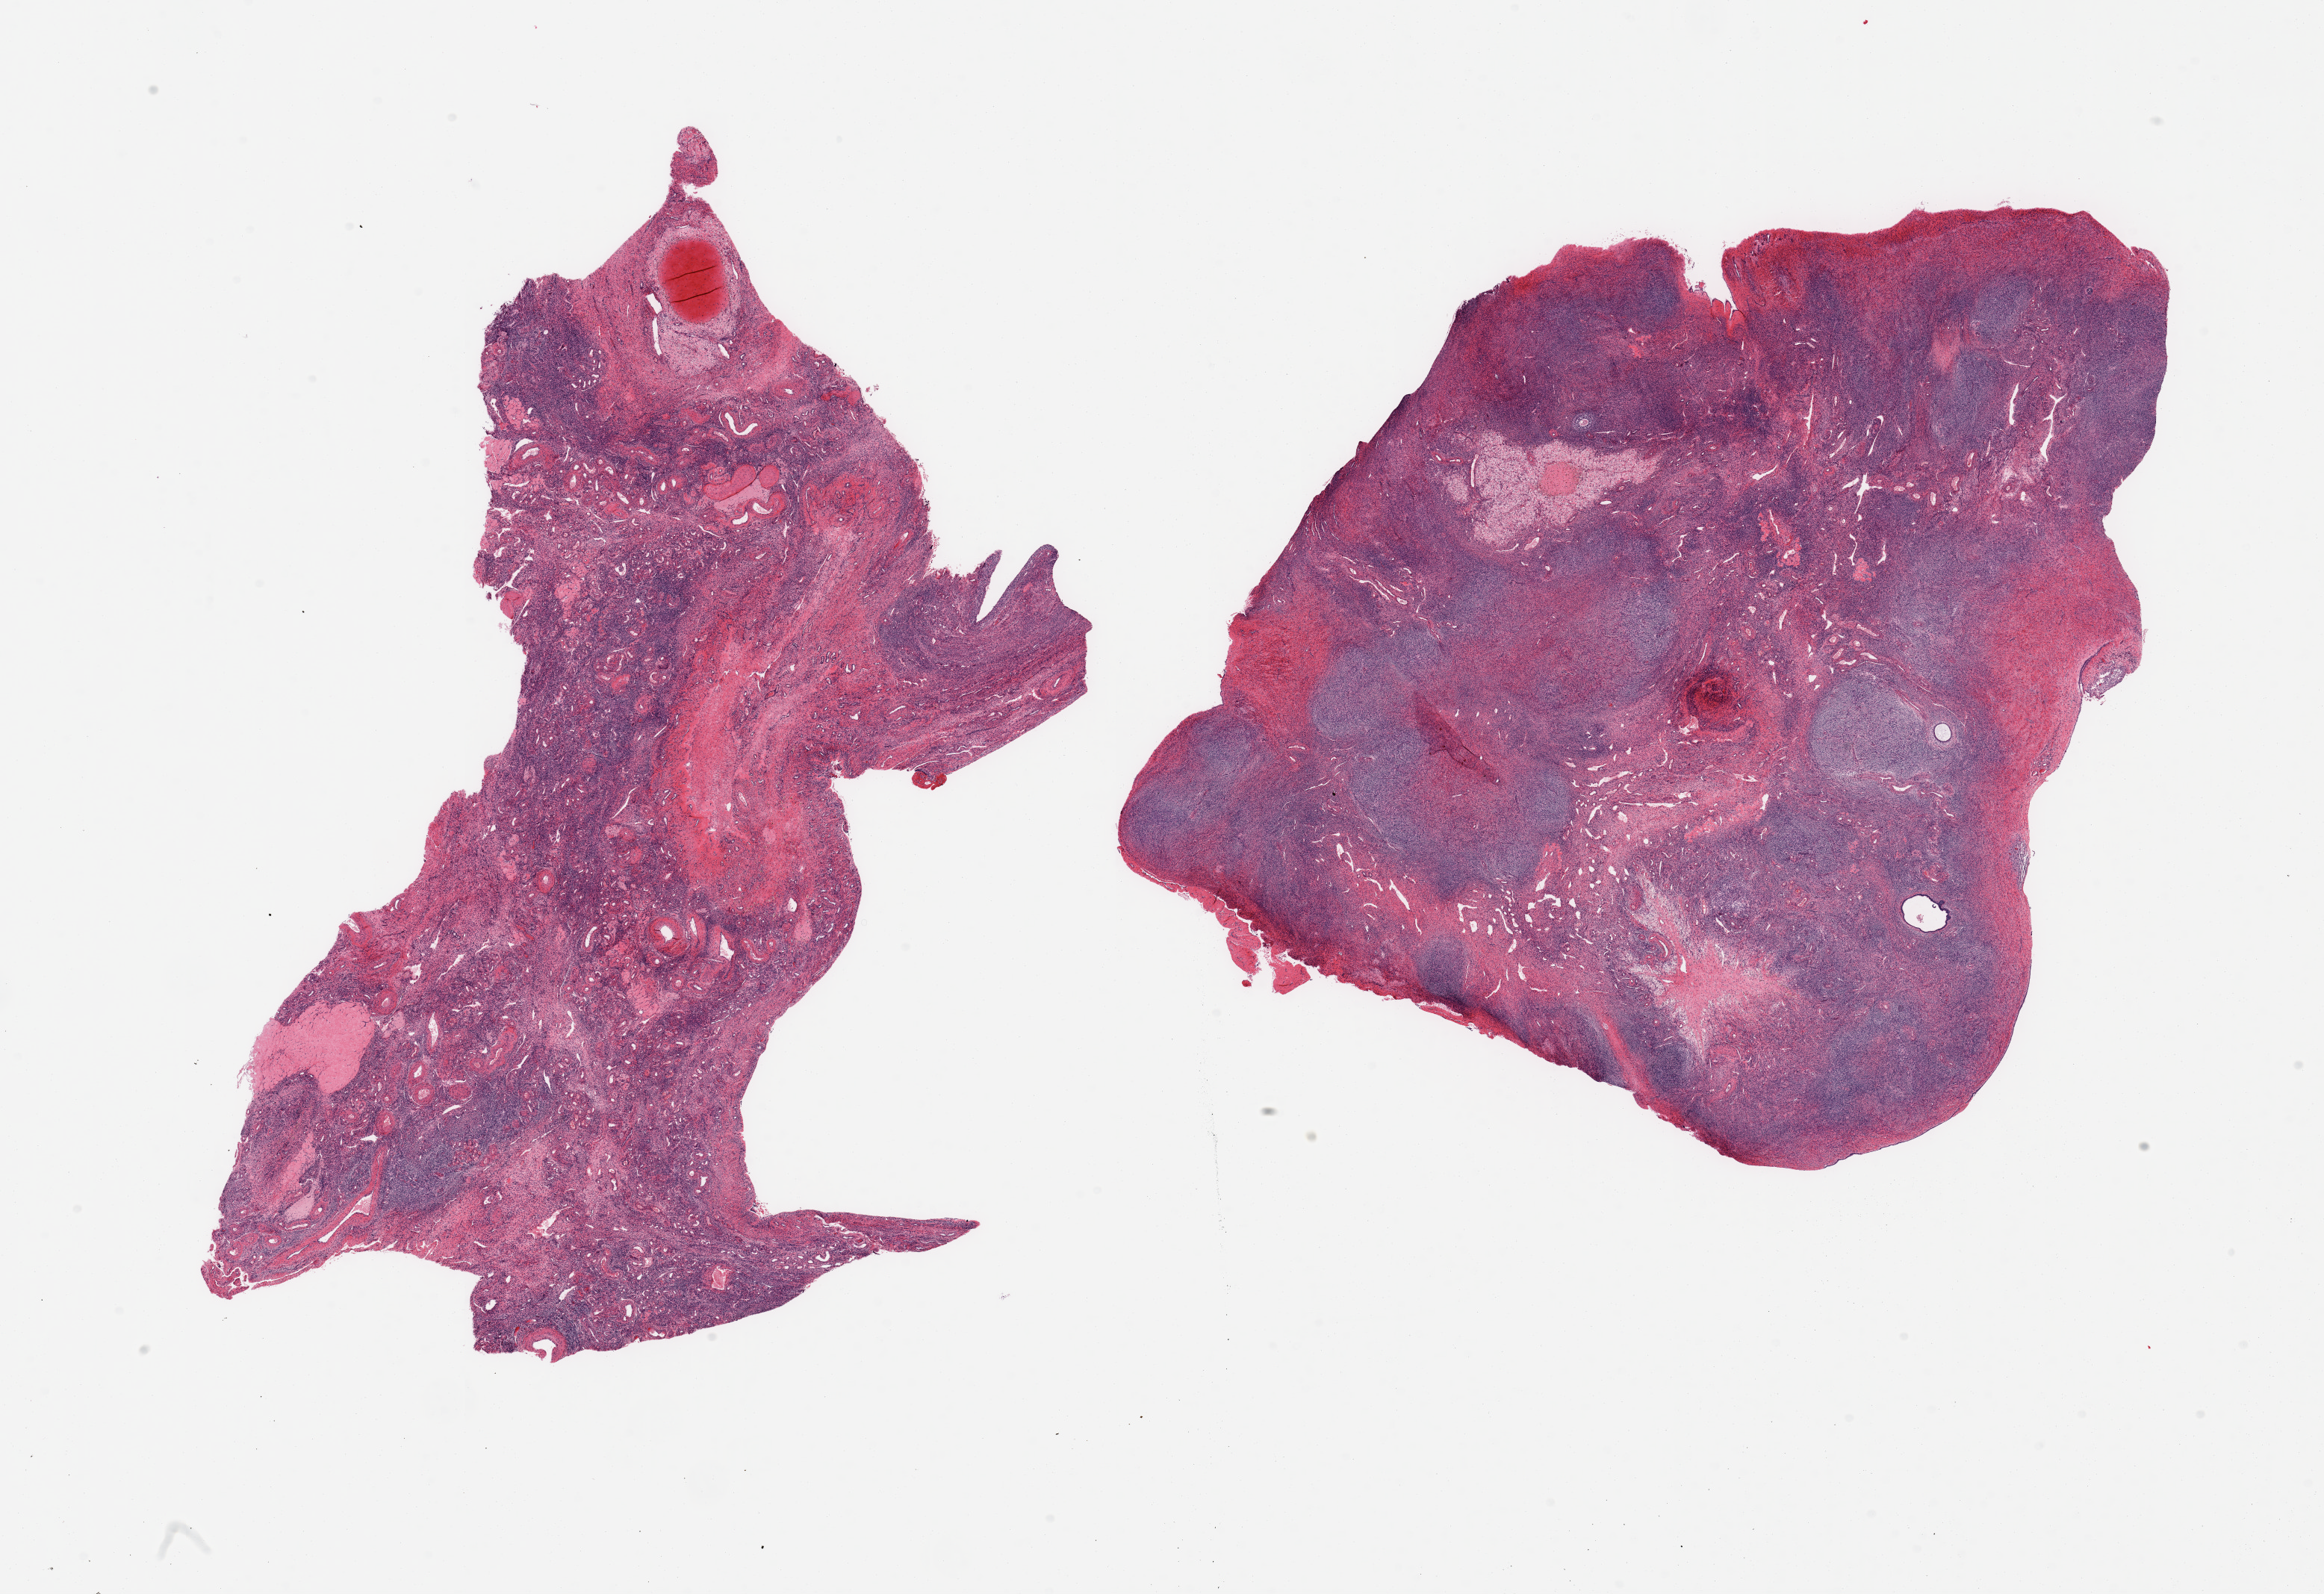
Digitized H&E-stained section, brightfield — shown as a low-resolution overview of the whole scanned area (about 24.6 x 16.9 mm, slide scanned at 20x); PAXgene-fixed, paraffin-embedded tissue; target tissue: ovary; tissue donor sample. Donor sex: female.
• reviewer comment on this tissue sample: 2 pieces; ovarian cortex with follicles, corpora lutea and corpora albicantia